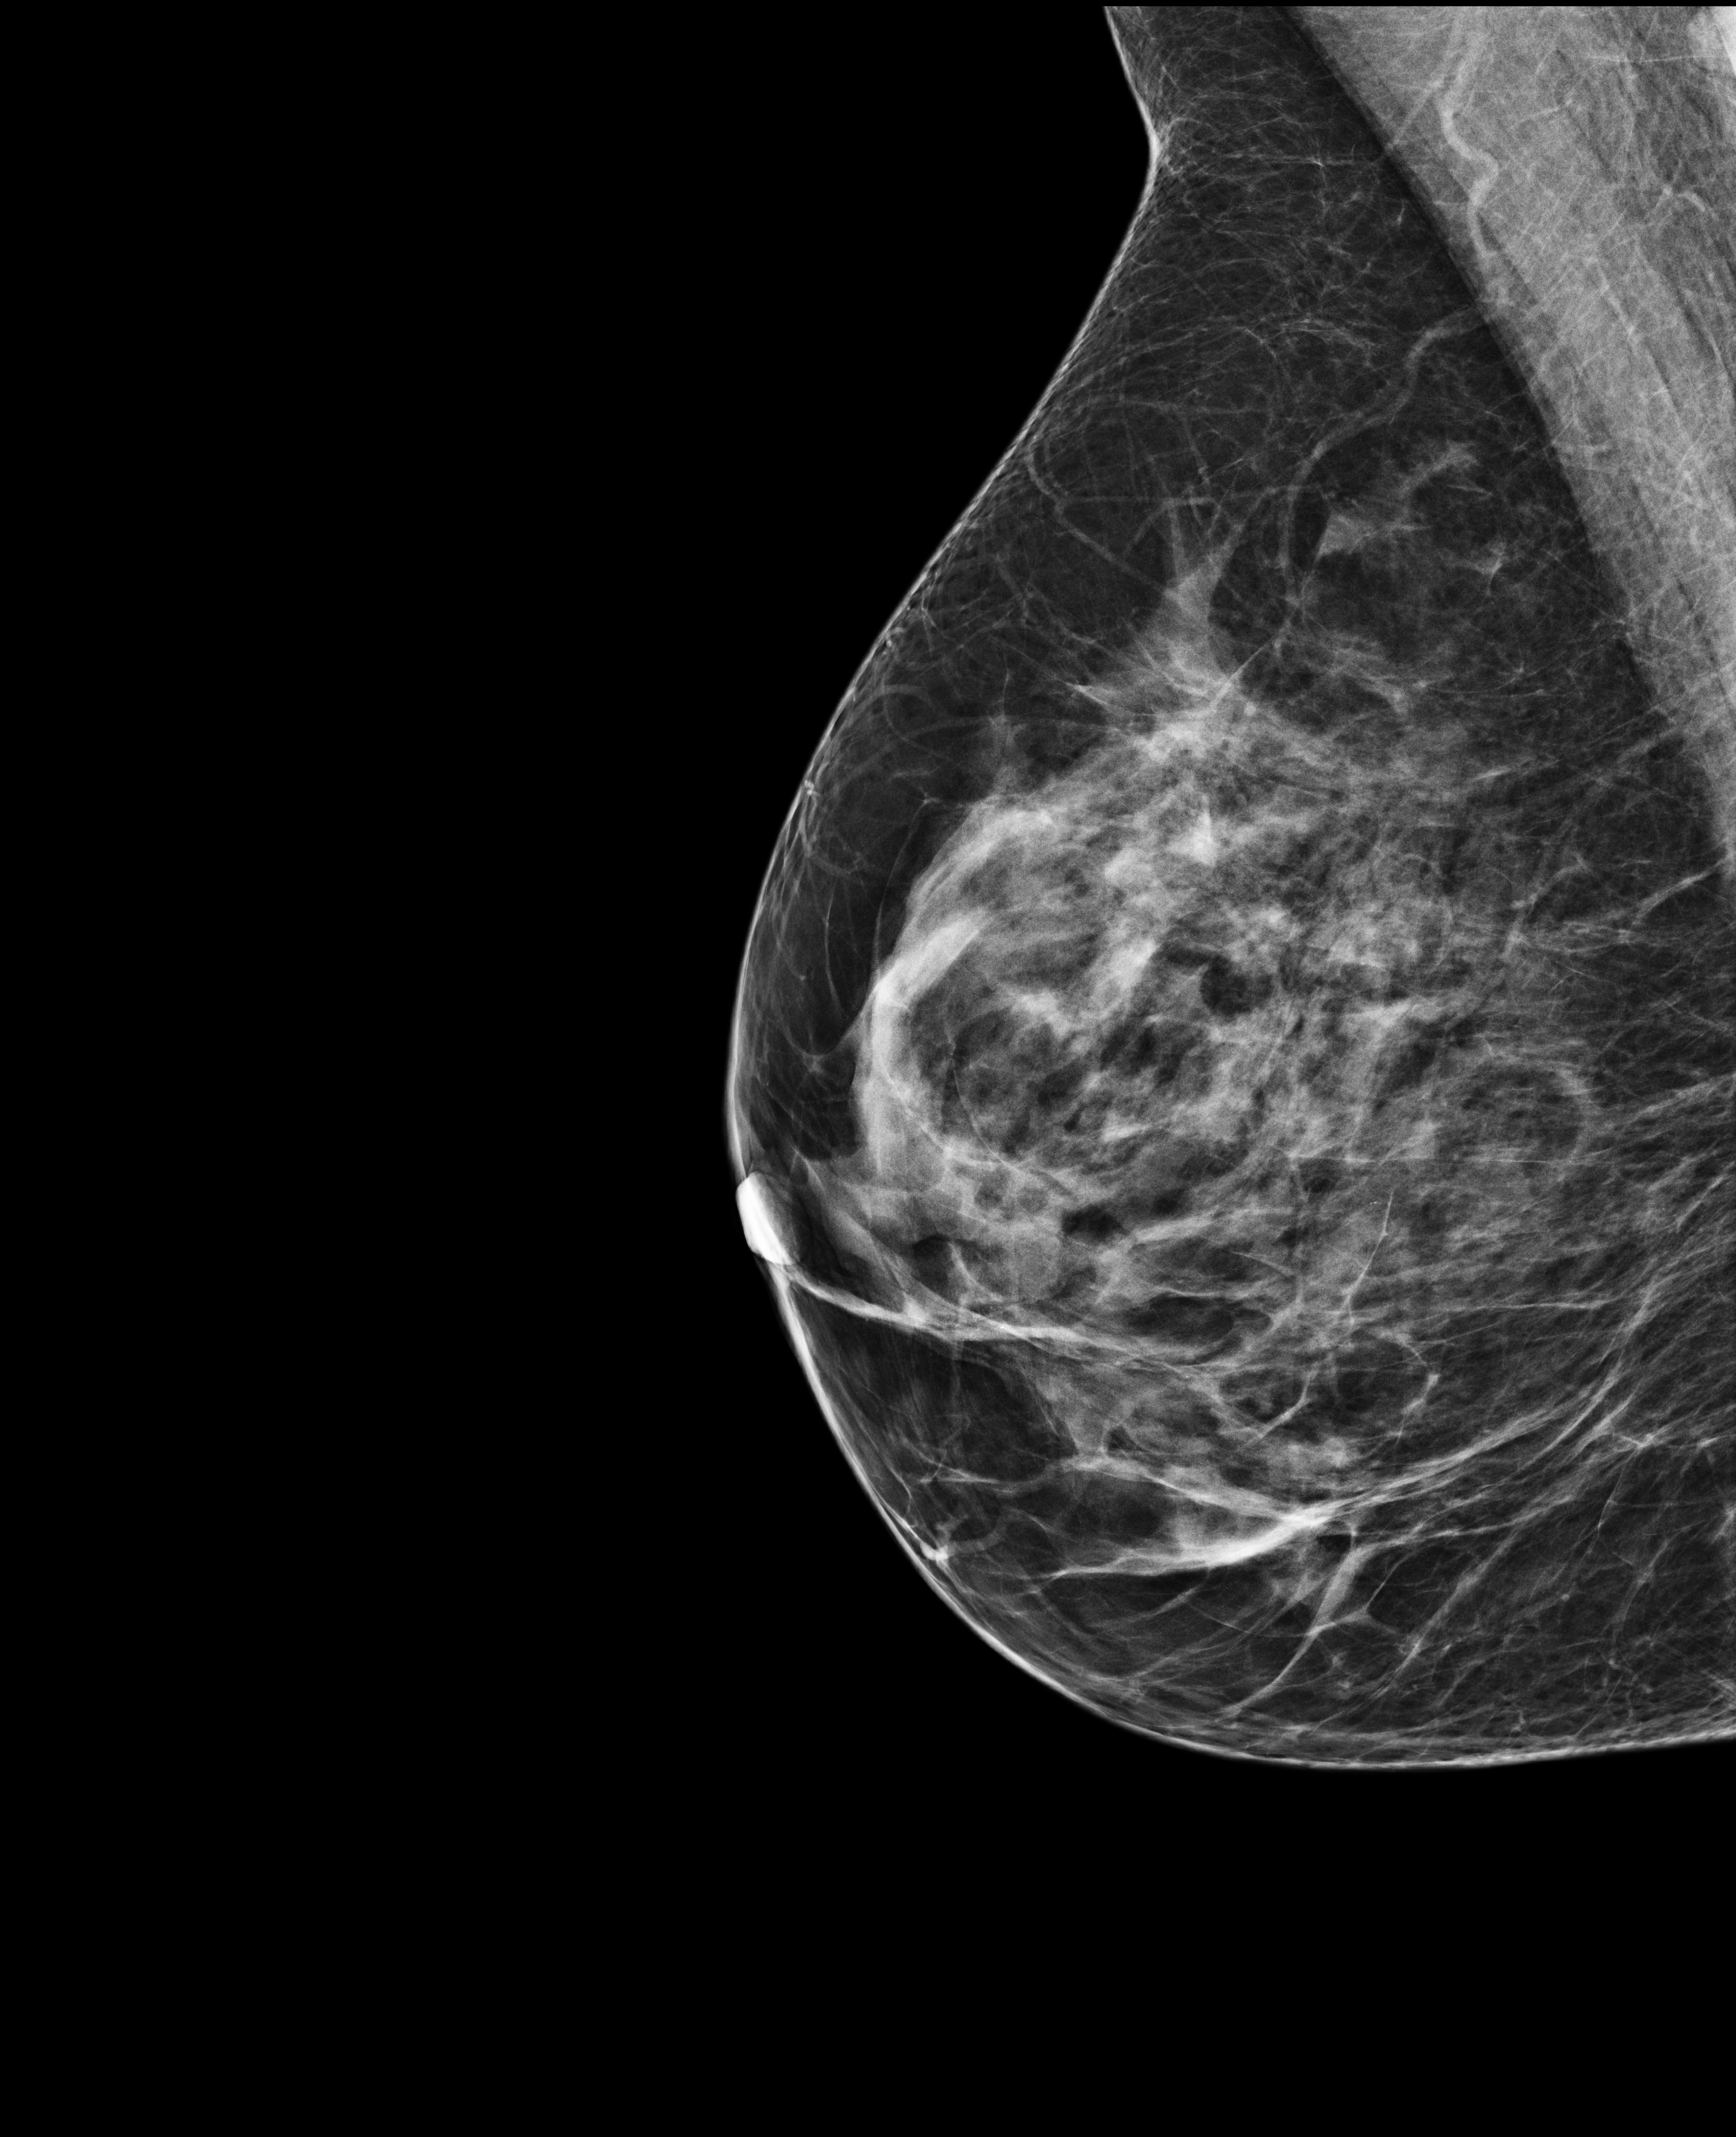
Screening examination; compressed breast thickness 53 mm; system: Selenia Dimensions. Patient aged 53 years (female).
Image type: full-field digital mammogram. Breast: right. Projection: MLO view. BI-RADS breast density category at the screening exam (both breasts, scale 1–4): 2. Final BI-RADS category for the screening round (tomosynthesis exam, both breasts): category 1. Recall: no recall after this screen.